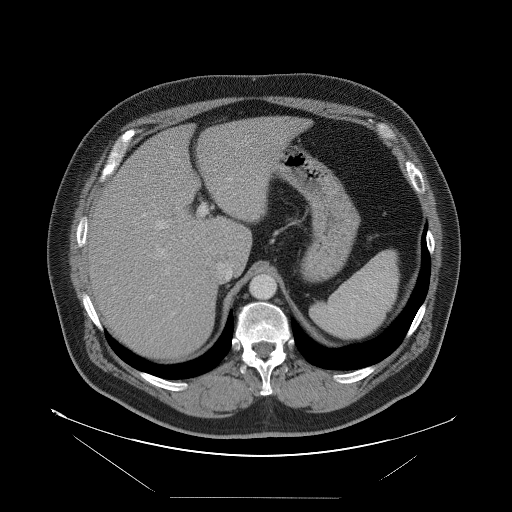
Contrast-enhanced abdominal CT, one axial slice; slice 69 of 114 in the series (ordered by position); 120 kVp; intravenous contrast given; soft-tissue window (W 400 / L 40 HU); 5 mm slice thickness; 512 × 512 image matrix, field of view 500 × 500 mm. Male patient, age 61 years. From the clinical record (not read from this slice): diagnosis: colorectal cancer liver metastases, imaged before liver resection; multiple liver metastases: no; largest metastasis: 6.5 cm; disease in both lobes: yes.
Outlined on this slice (outlined manually by an expert reader):
- hepatic veins: bounding box <157,177,234,281> (left, top, right, bottom; pixels)
- liver: <88,117,301,358>
- planned liver remnant (the part of the liver to remain after resection): <145,117,301,273>
- portal vein (with intrahepatic branches): <141,205,207,302>